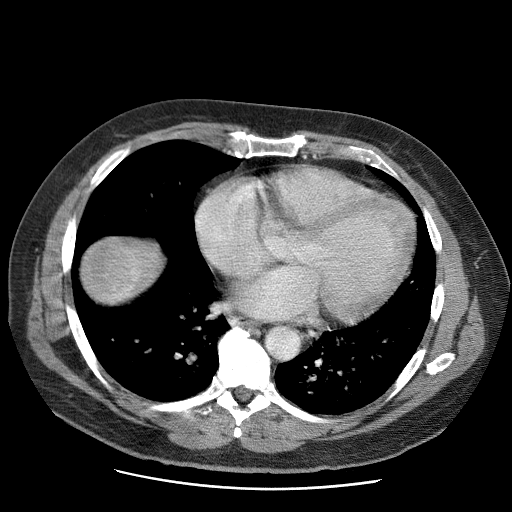
Contrast-enhanced abdominal CT (liver protocol), one axial slice; position 68 of 81 along the scan axis; 120 kVp; soft-tissue window (W 400 / L 40 HU); 2.5 mm slice thickness; 512 × 512 image matrix. From the clinical record (not read from this slice): diagnosis: hepatocellular carcinoma (patient treated with transarterial chemoembolisation; whether this scan precedes or follows treatment is not stated here); TNM stage (as recorded): Stage-IIIA; Child-Pugh class: A.
Annotated regions visible in this slice (semi-automatic segmentation, software-assisted and operator-edited):
- liver parenchyma outside the tumour (the mass and vessels are separate outlines, so this box may not span the whole liver): box from (x=84, y=242) to (x=160, y=300) px
- mass: (x=80, y=238)–(x=142, y=304)